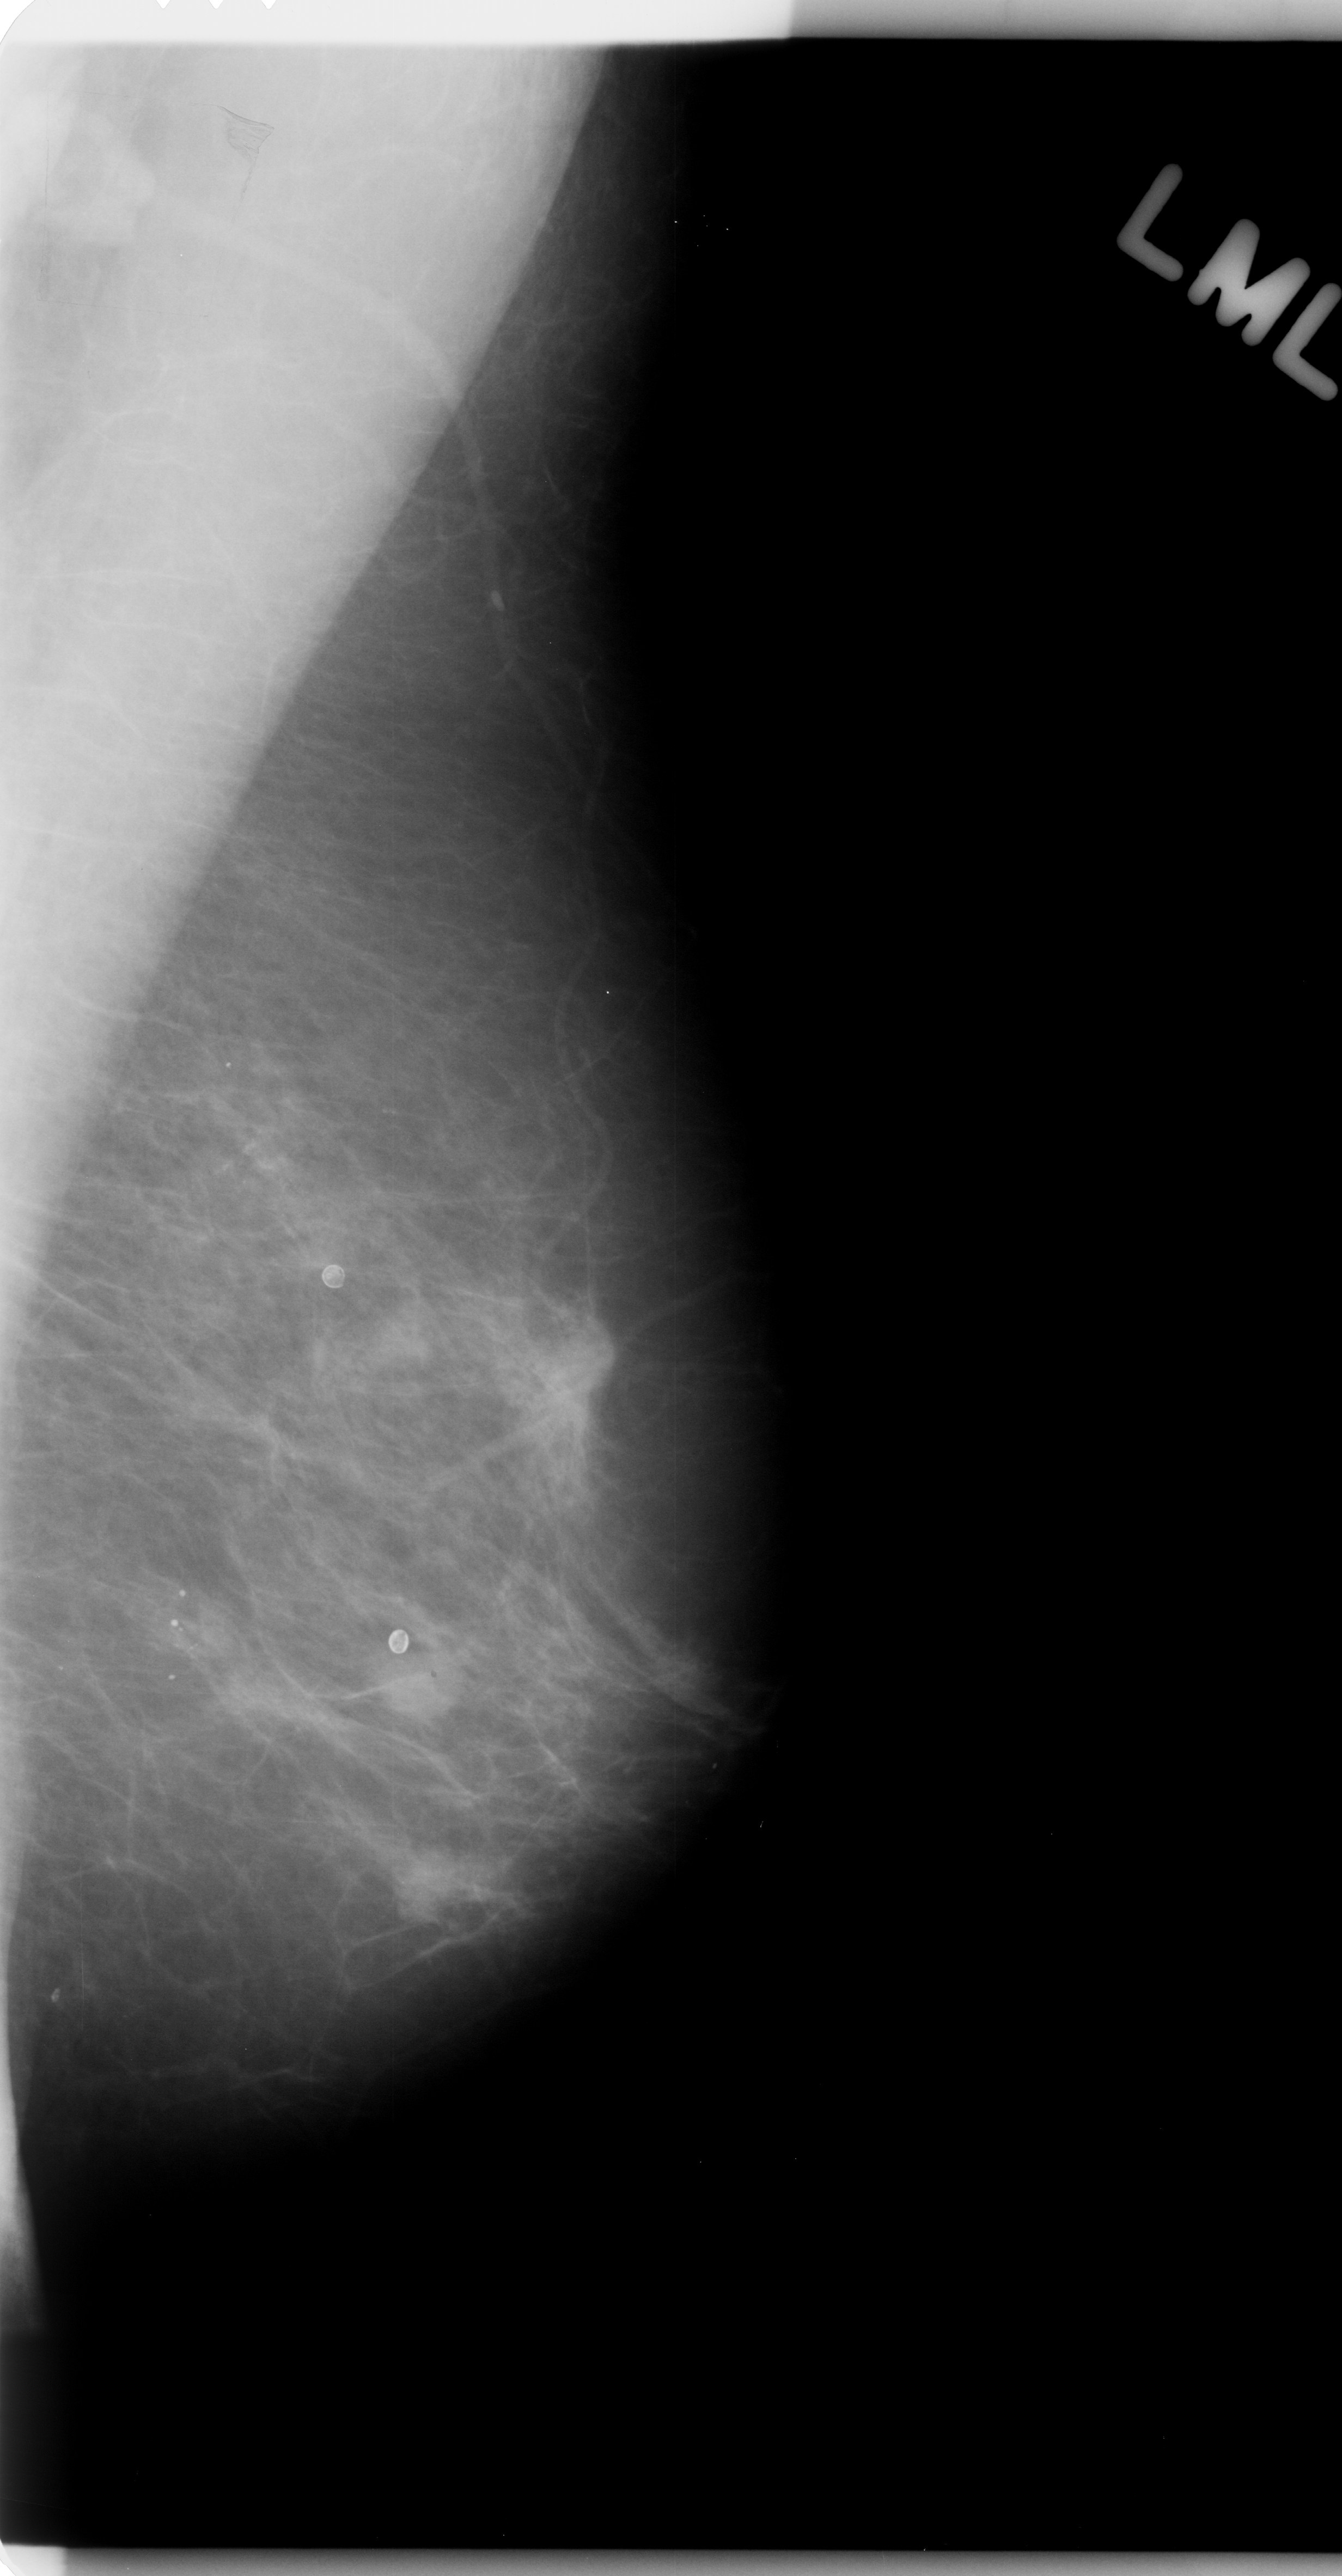
Scanned film-screen mammogram, left breast, MLO view, breast composition: almost entirely fatty (BI-RADS density category 1 of 4).
Abnormality record for this image: Finding 1 of 3: mass, shape oval, margins microlobulated; BI-RADS assessment category 4; subtlety rating 5 on a 1 (subtle) to 5 (obvious) scale; pathology (as recorded): malignant. Finding 2 of 3: mass, shape oval, margins microlobulated; BI-RADS assessment category 4; pathology (as recorded): malignant. Finding 3 of 3: mass, shape oval, margins microlobulated; BI-RADS assessment category 4; pathology result (as recorded, not read from the image): malignant.